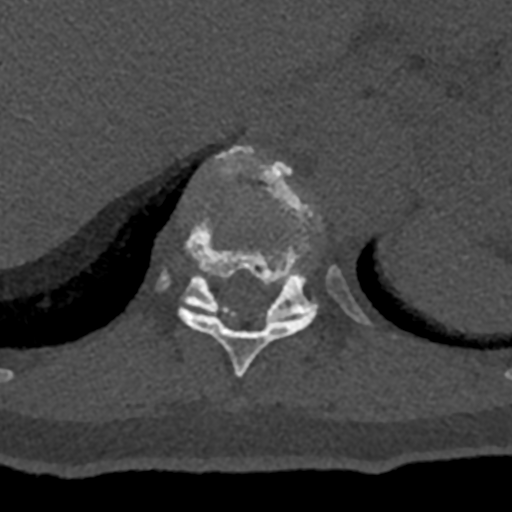
CT including the spine, one axial slice; reconstruction kernel Br40s/3; bone window (W 1800 / L 400 HU); 0.5 mm slice thickness; 512 × 512 image matrix, field of view 160 × 160 mm. Male patient, age 74 years. Case-level facts recorded for this patient, not image findings: primary cancer: renal; vertebrae with lytic lesions (as recorded): T10, L1, L2, L3, L4, L5.
Annotated regions visible in this slice (semi-automatically segmented with operator editing):
- T10 vertebra: bounding box <178,148,316,378> (left, top, right, bottom; pixels)
- T11 vertebra: <156,152,371,326>